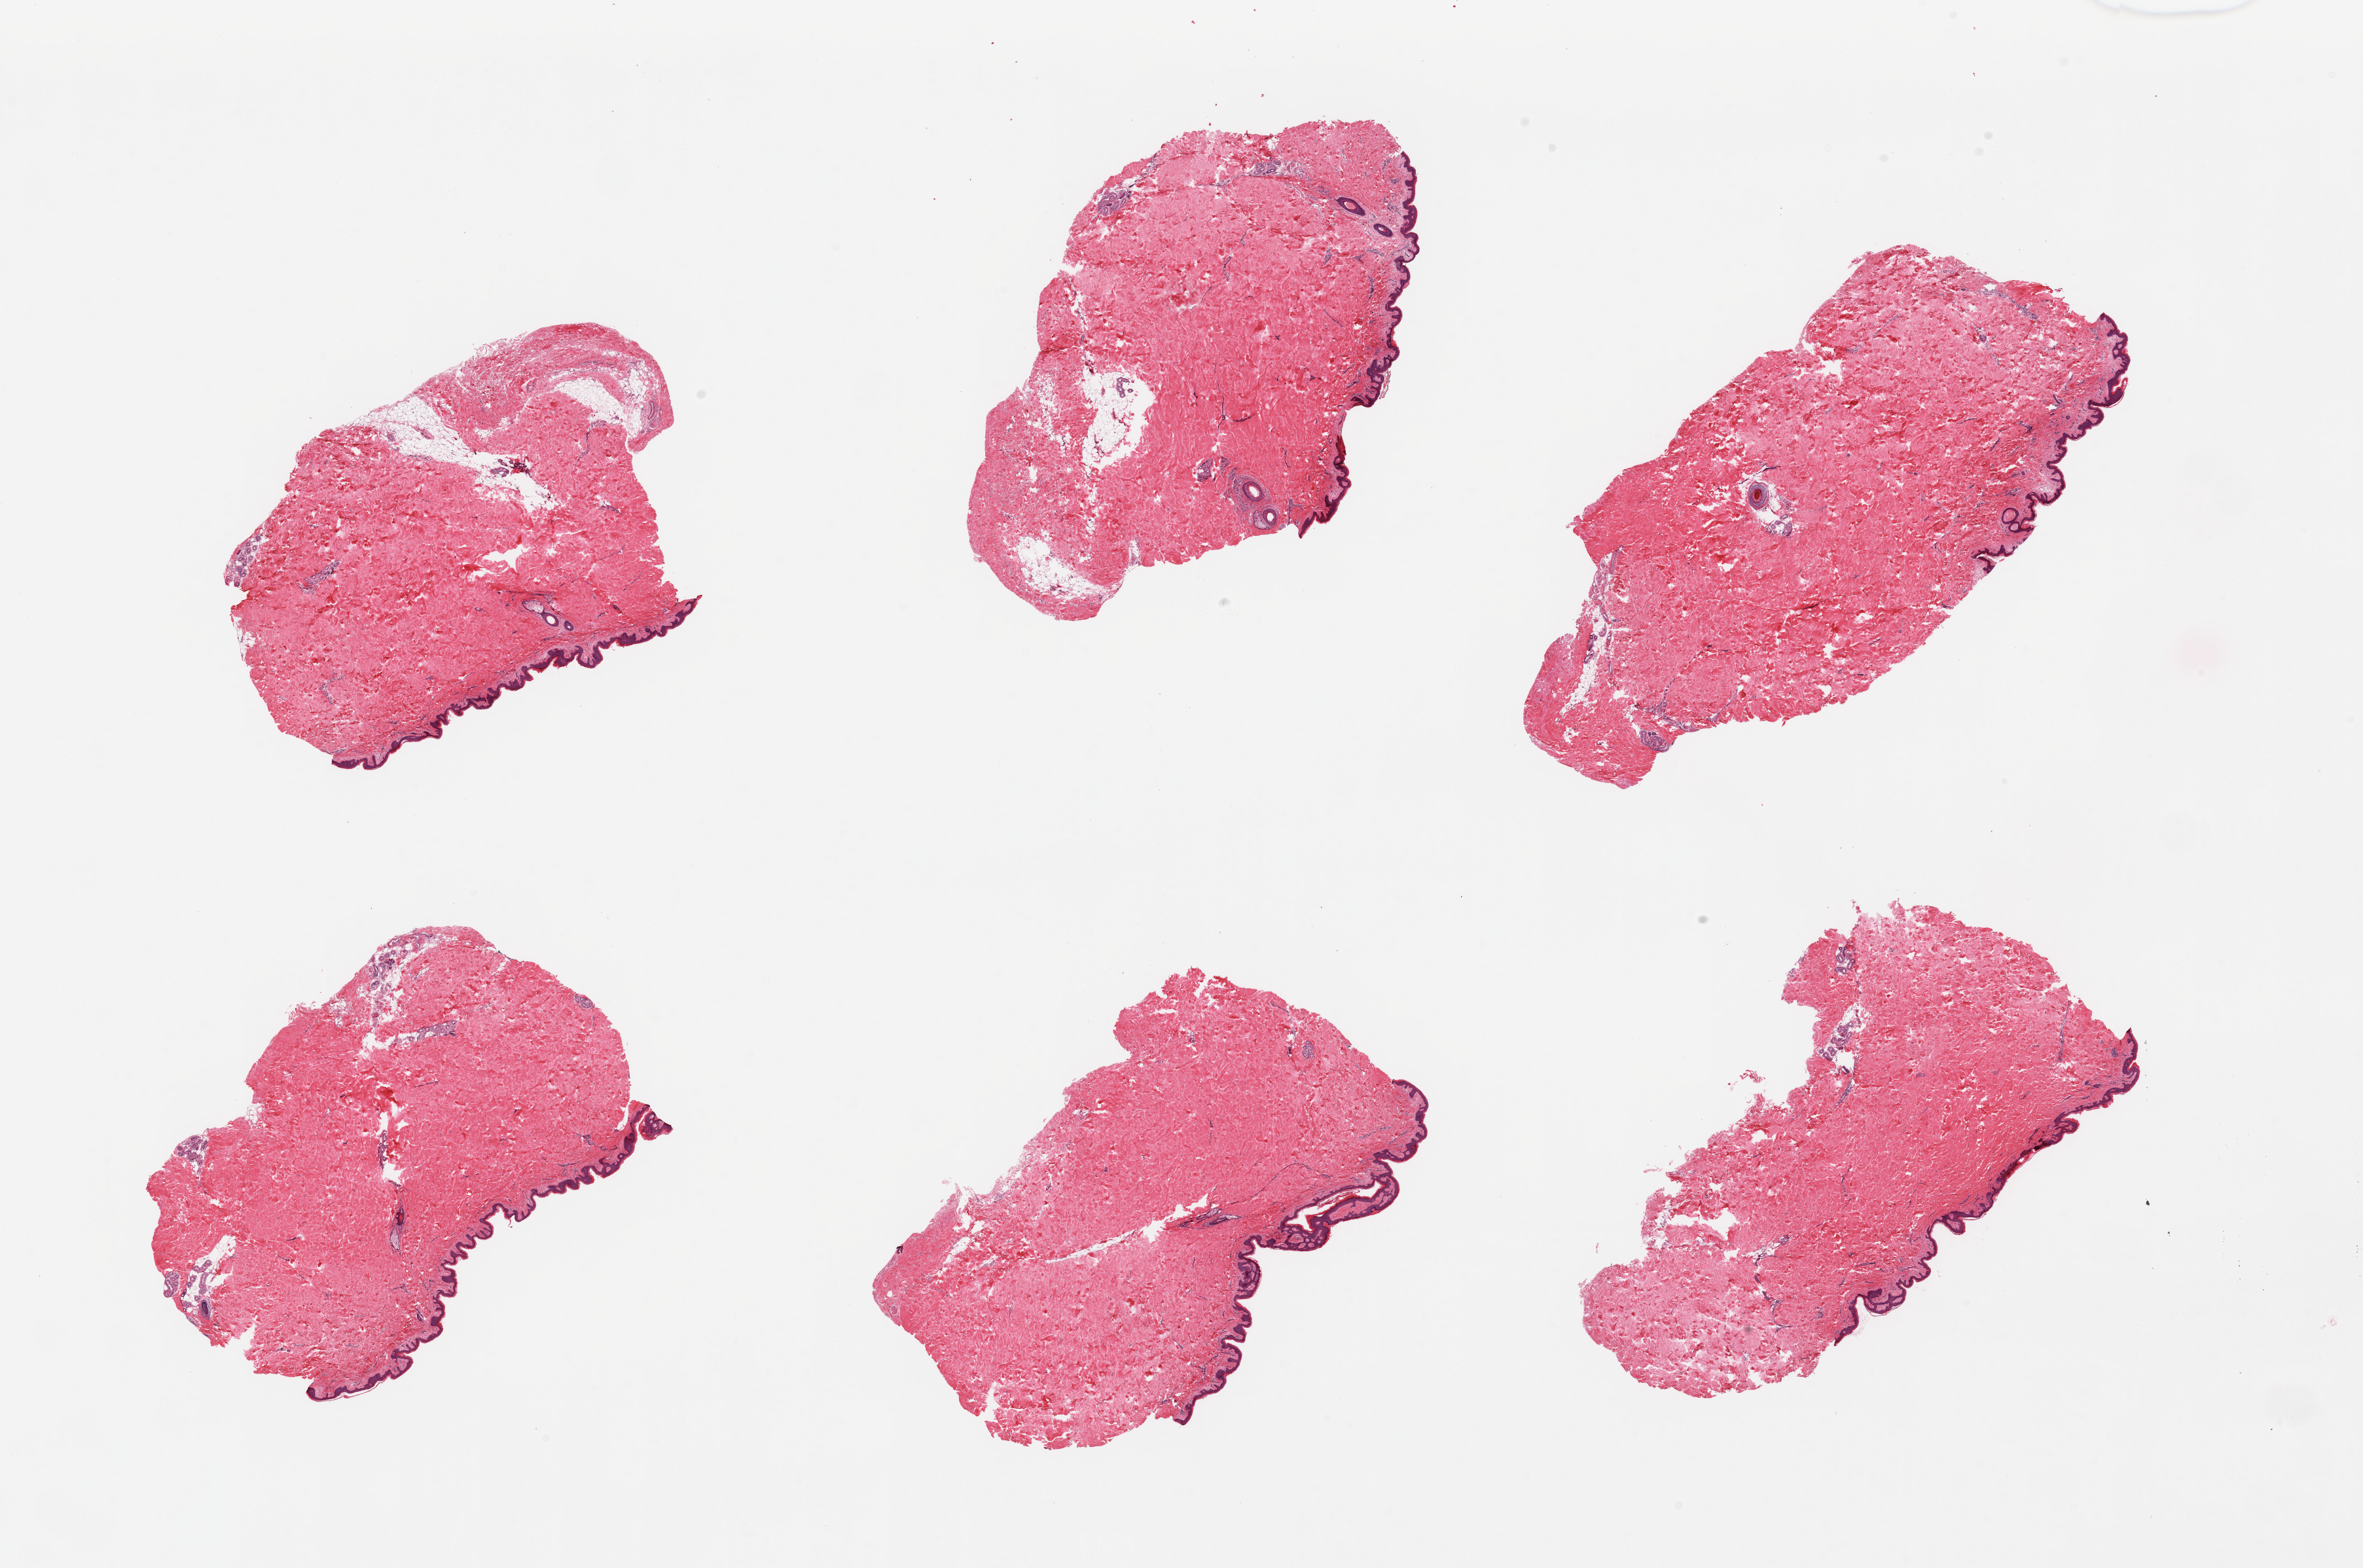
Digitized H&E-stained section, whole scanned area (about 28.5 x 18.9 mm) shown as a low-resolution overview, PAXgene-fixed, paraffin-embedded tissue, target tissue: skin of suprapubic region, donor tissue sample. Donor: male.
Pathologist's review note for this sample: 6 pieces; well trimmed, include <10% internal fat.